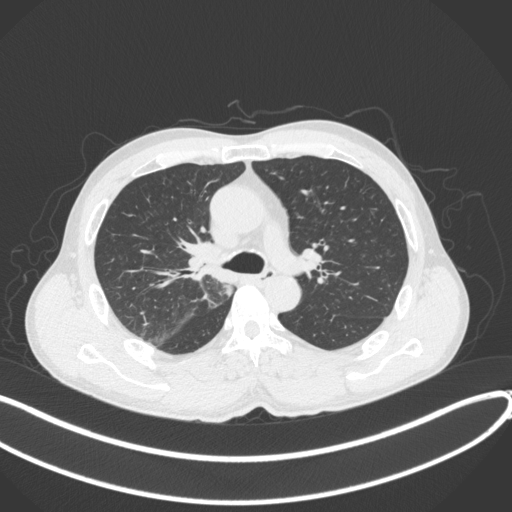
Chest CT, one axial slice. Position 255 of 409 along the scan axis. 120 kVp. Lung window (W 1500 / L -600 HU). 1 mm slice thickness. 512 × 512 image matrix, field of view 400 × 400 mm. Patient: male, 53 years. From the clinical record (not read from this slice): clinical TNM (as recorded): T1b N0 M0.
Structures marked on this image (rectangle marked by the reading radiologist):
- lung tumour (recorded histology: squamous cell carcinoma): bounding box [x1, y1, x2, y2] px = [183, 237, 232, 286]